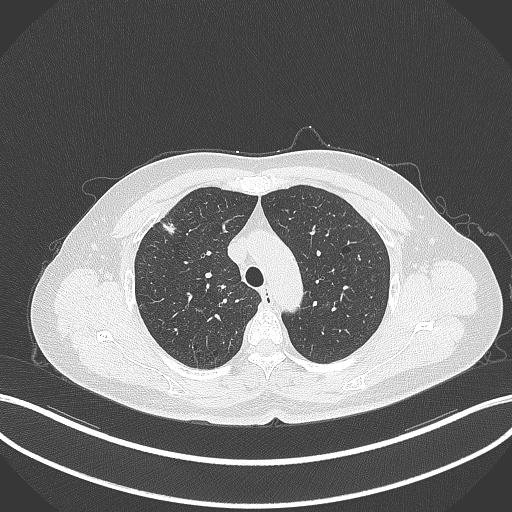
Chest CT, one axial slice. Slice 275 of 353 in the series (ordered by position). Reconstruction kernel B70f. 120 kVp. Lung window (W 1500 / L -600 HU). 512 × 512 image matrix. Female patient, age 56 years. From the clinical record (not read from this slice): clinical TNM (as recorded): T1c N0 M0.
Structures marked on this image (bounding box drawn by a radiologist):
- lung tumour (recorded histology: adenocarcinoma): bounding box [x1, y1, x2, y2] px = [157, 217, 178, 236]